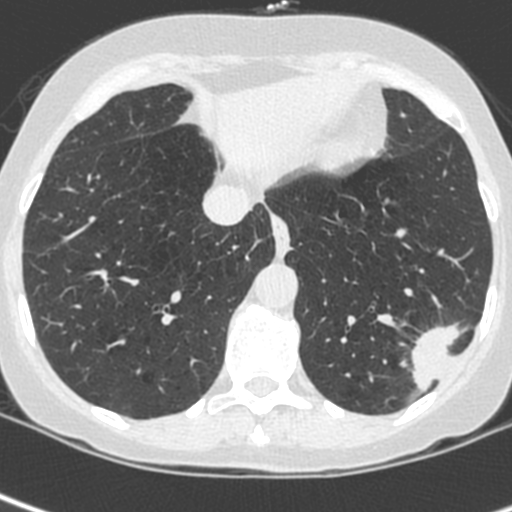
Chest CT (low-dose screening protocol), one axial image, baseline screening round, lung window (W 1500 / L -600 HU), 1.3 mm slice thickness, standard (soft-tissue) reconstruction kernel (C), 120 kVp, slice 172 of 252 in the series. Female, age 56 years at enrolment.
Expert-annotated lung lesion, bounding box (x1, y1, x2, y2) in pixels: (405, 317, 476, 388). Screening reader's record for this exam (one nodule recorded; not confirmed to be the boxed lesion): non-calcified nodule or mass ≥4 mm, left lower lobe, 37 × 29 mm, spiculated (stellate) margins, ground glass attenuation. Official screen result: positive, change unspecified: nodule(s) >= 4 mm or enlarging nodule(s), mass(es), or other non-specific abnormalities suspicious for lung cancer. Later outcome: lung cancer diagnosed 91 days after this screen — squamous cell carcinoma, NOS, left lower lobe, poorly differentiated (G3), stage IIIA (AJCC 6th edition), 35 mm at pathology.